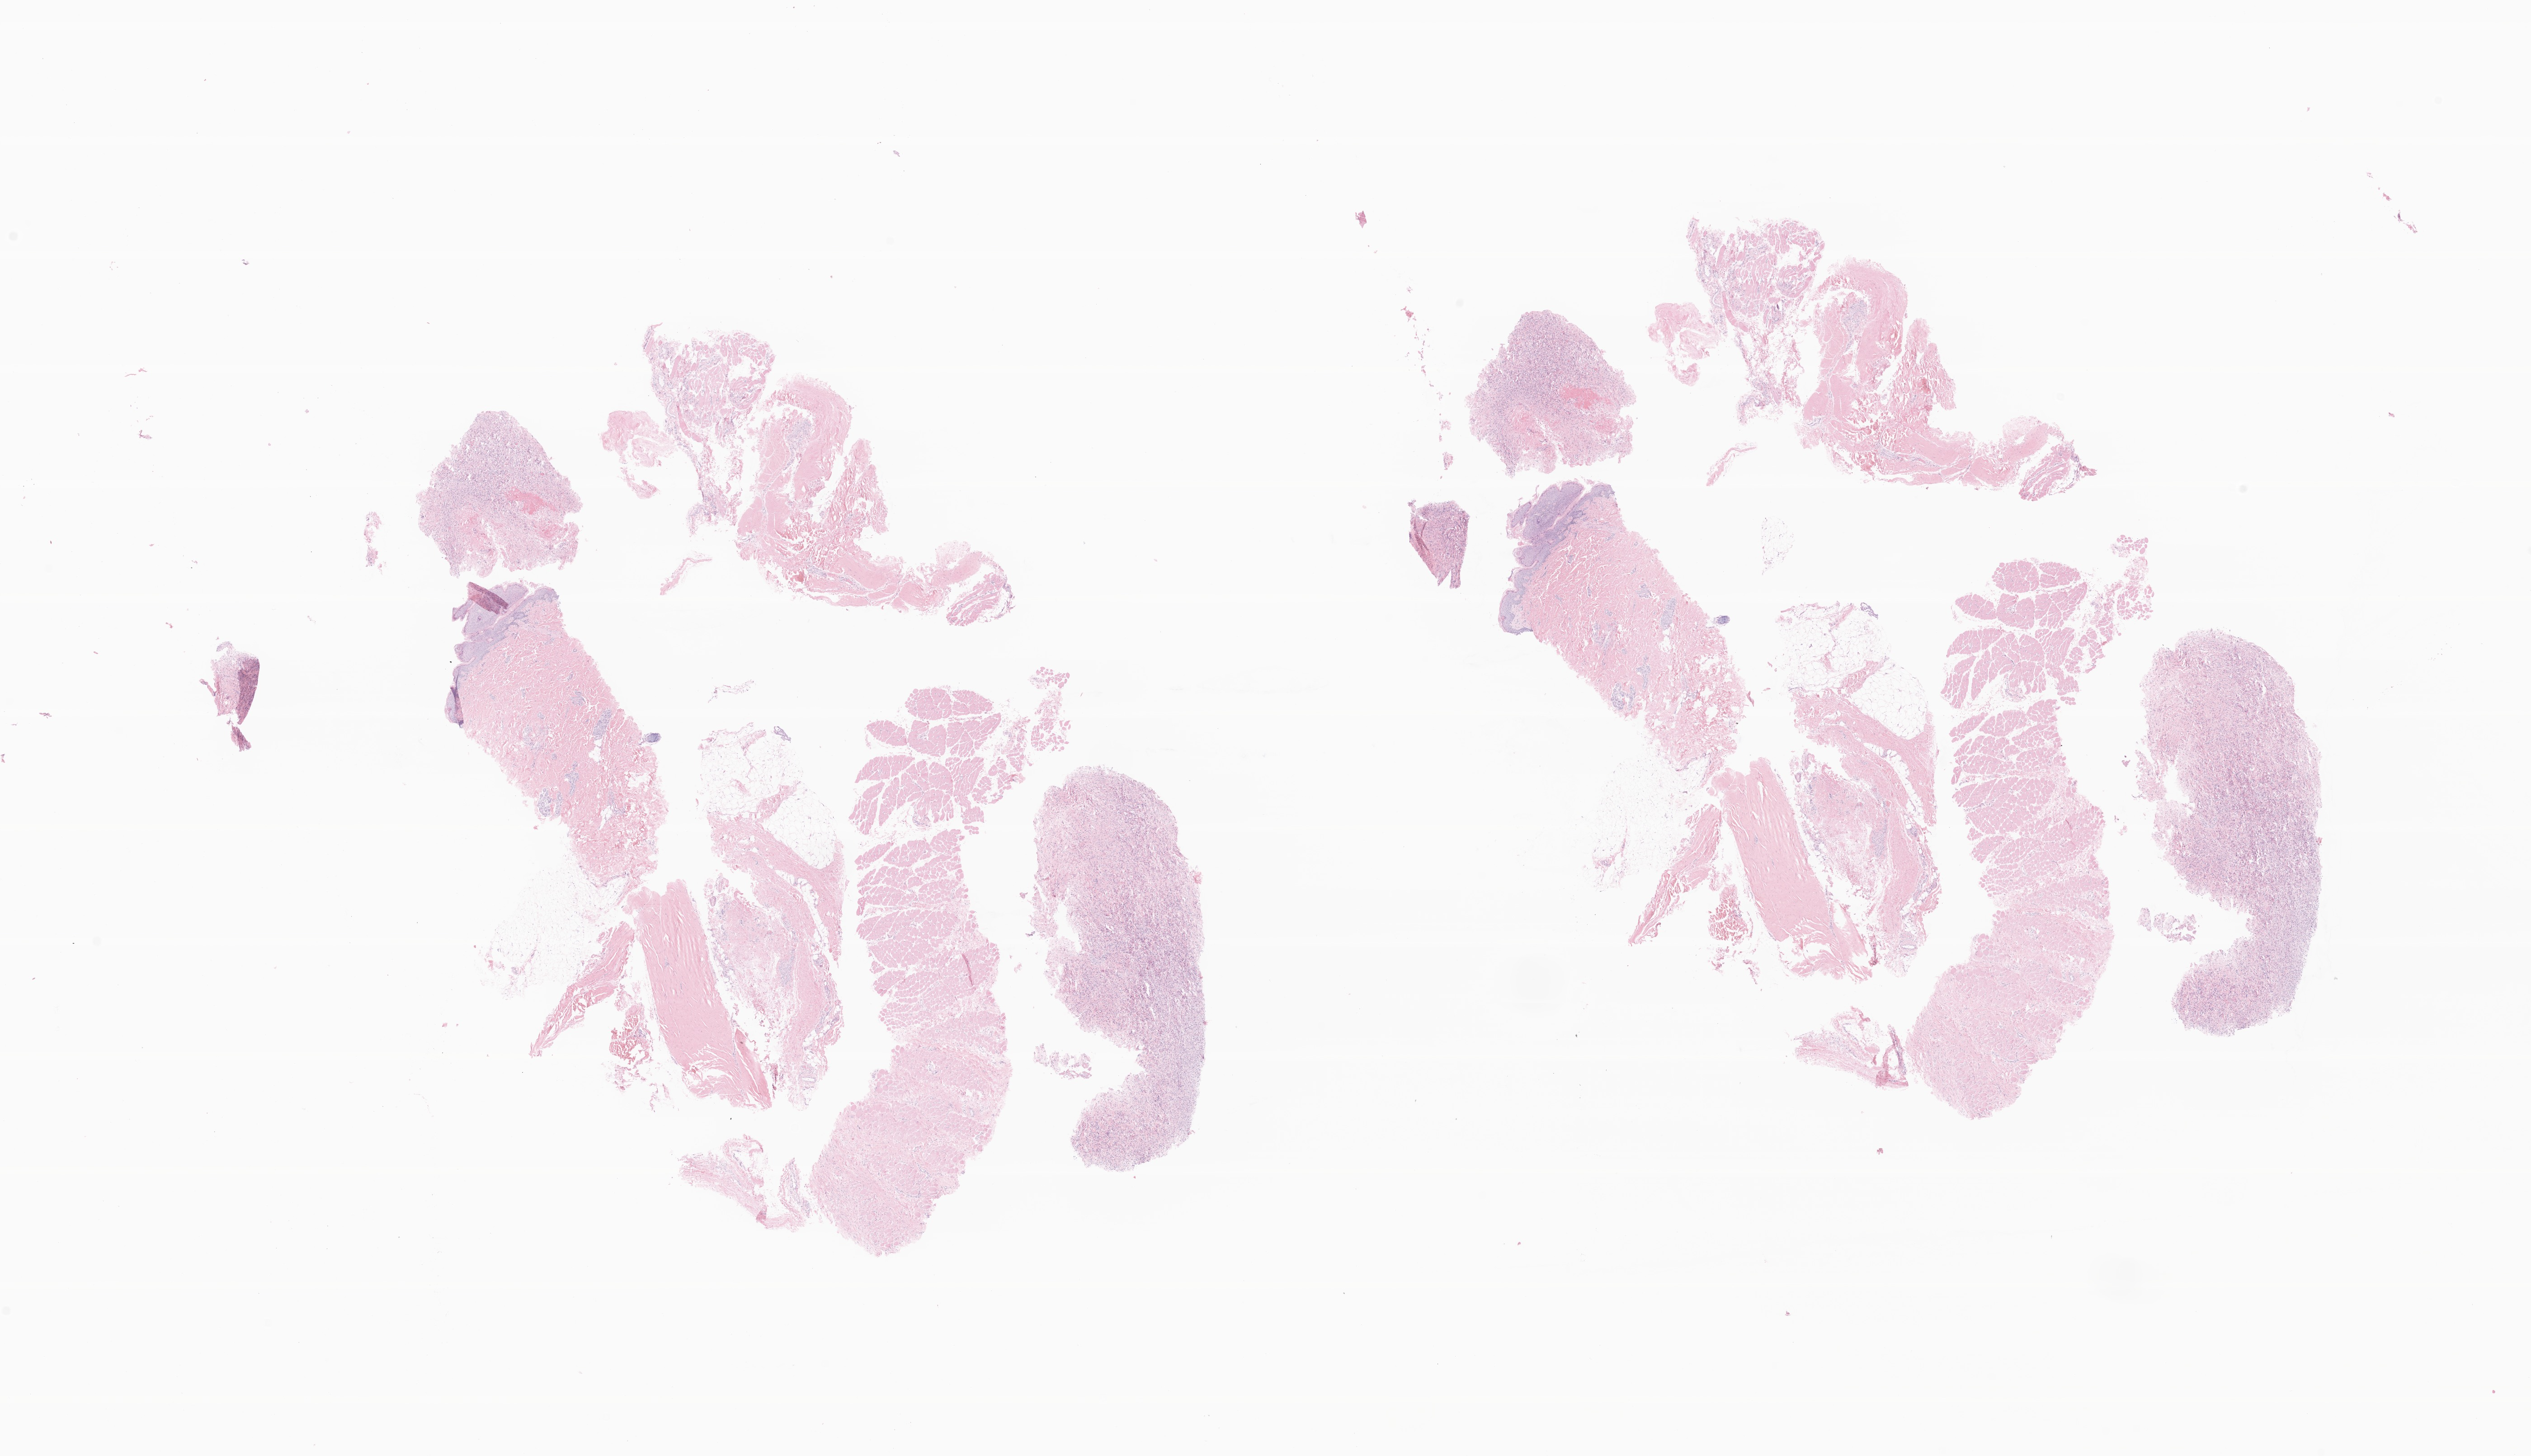
Digitized hematoxylin and eosin (H&E)-stained section of tumor tissue from the spinal cord, low-resolution overview of the scanned area, about 23.6 x 13.6 mm, formalin-fixed paraffin-embedded section. Patient: female, age 668 days (about 1.8 years).
Diagnosis: Spindle cell rhabdomyosarcoma.